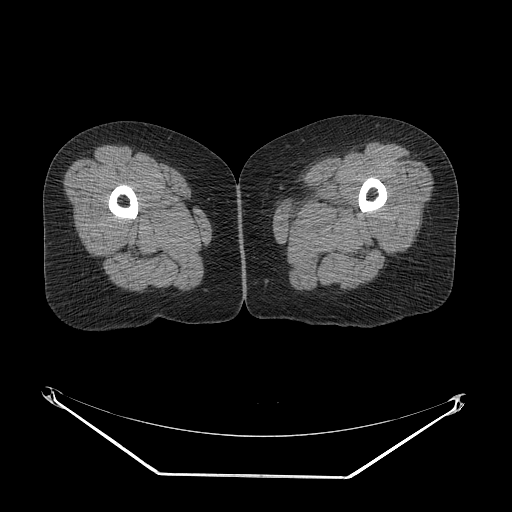
CT of an extremity soft-tissue mass (from a PET/CT study), one axial slice. Position 1 of 267 along the scan axis. 140 kVp. Soft-tissue window (W 400 / L 40 HU). 3.75 mm slice thickness. 512 × 512 image matrix. Female patient. From the clinical record (not read from this slice): histological type: myxofibrosarcoma; grade: intermediate; site of the primary tumour: left thigh.
Annotated regions visible in this slice (expert contour drawn on MRI and transferred to this co-registered scan by the dataset authors):
- gross tumour volume including surrounding oedema: bounding box [x1, y1, x2, y2] px = [294, 210, 343, 229]